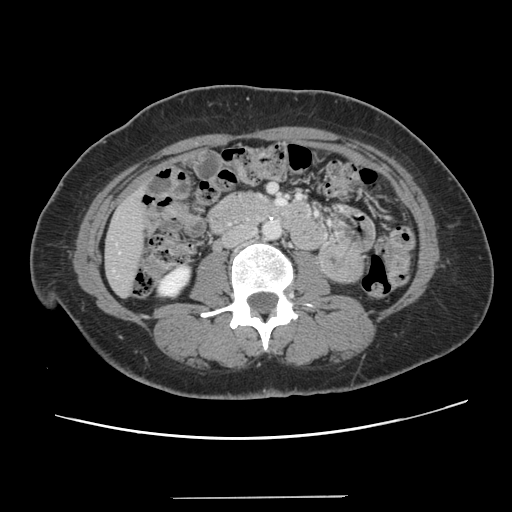
Contrast-enhanced abdominal CT, one axial slice. Slice 30 of 141 in the series (ordered by position). 120 kVp. Intravenous contrast given. Soft-tissue window (W 400 / L 40 HU). 2.5 mm slice thickness. 512 × 512 image matrix, field of view 366 × 366 mm. Female patient, age 53 years. From the clinical record (not read from this slice): diagnosis: colorectal cancer liver metastases, imaged before liver resection; multiple liver metastases: no; largest metastasis: 14.5 cm.
Annotated regions visible in this slice (manually delineated by an expert):
- liver: box from (x=106, y=193) to (x=145, y=295) px
- planned liver remnant (the part of the liver to remain after resection): (x=106, y=206)–(x=144, y=295)